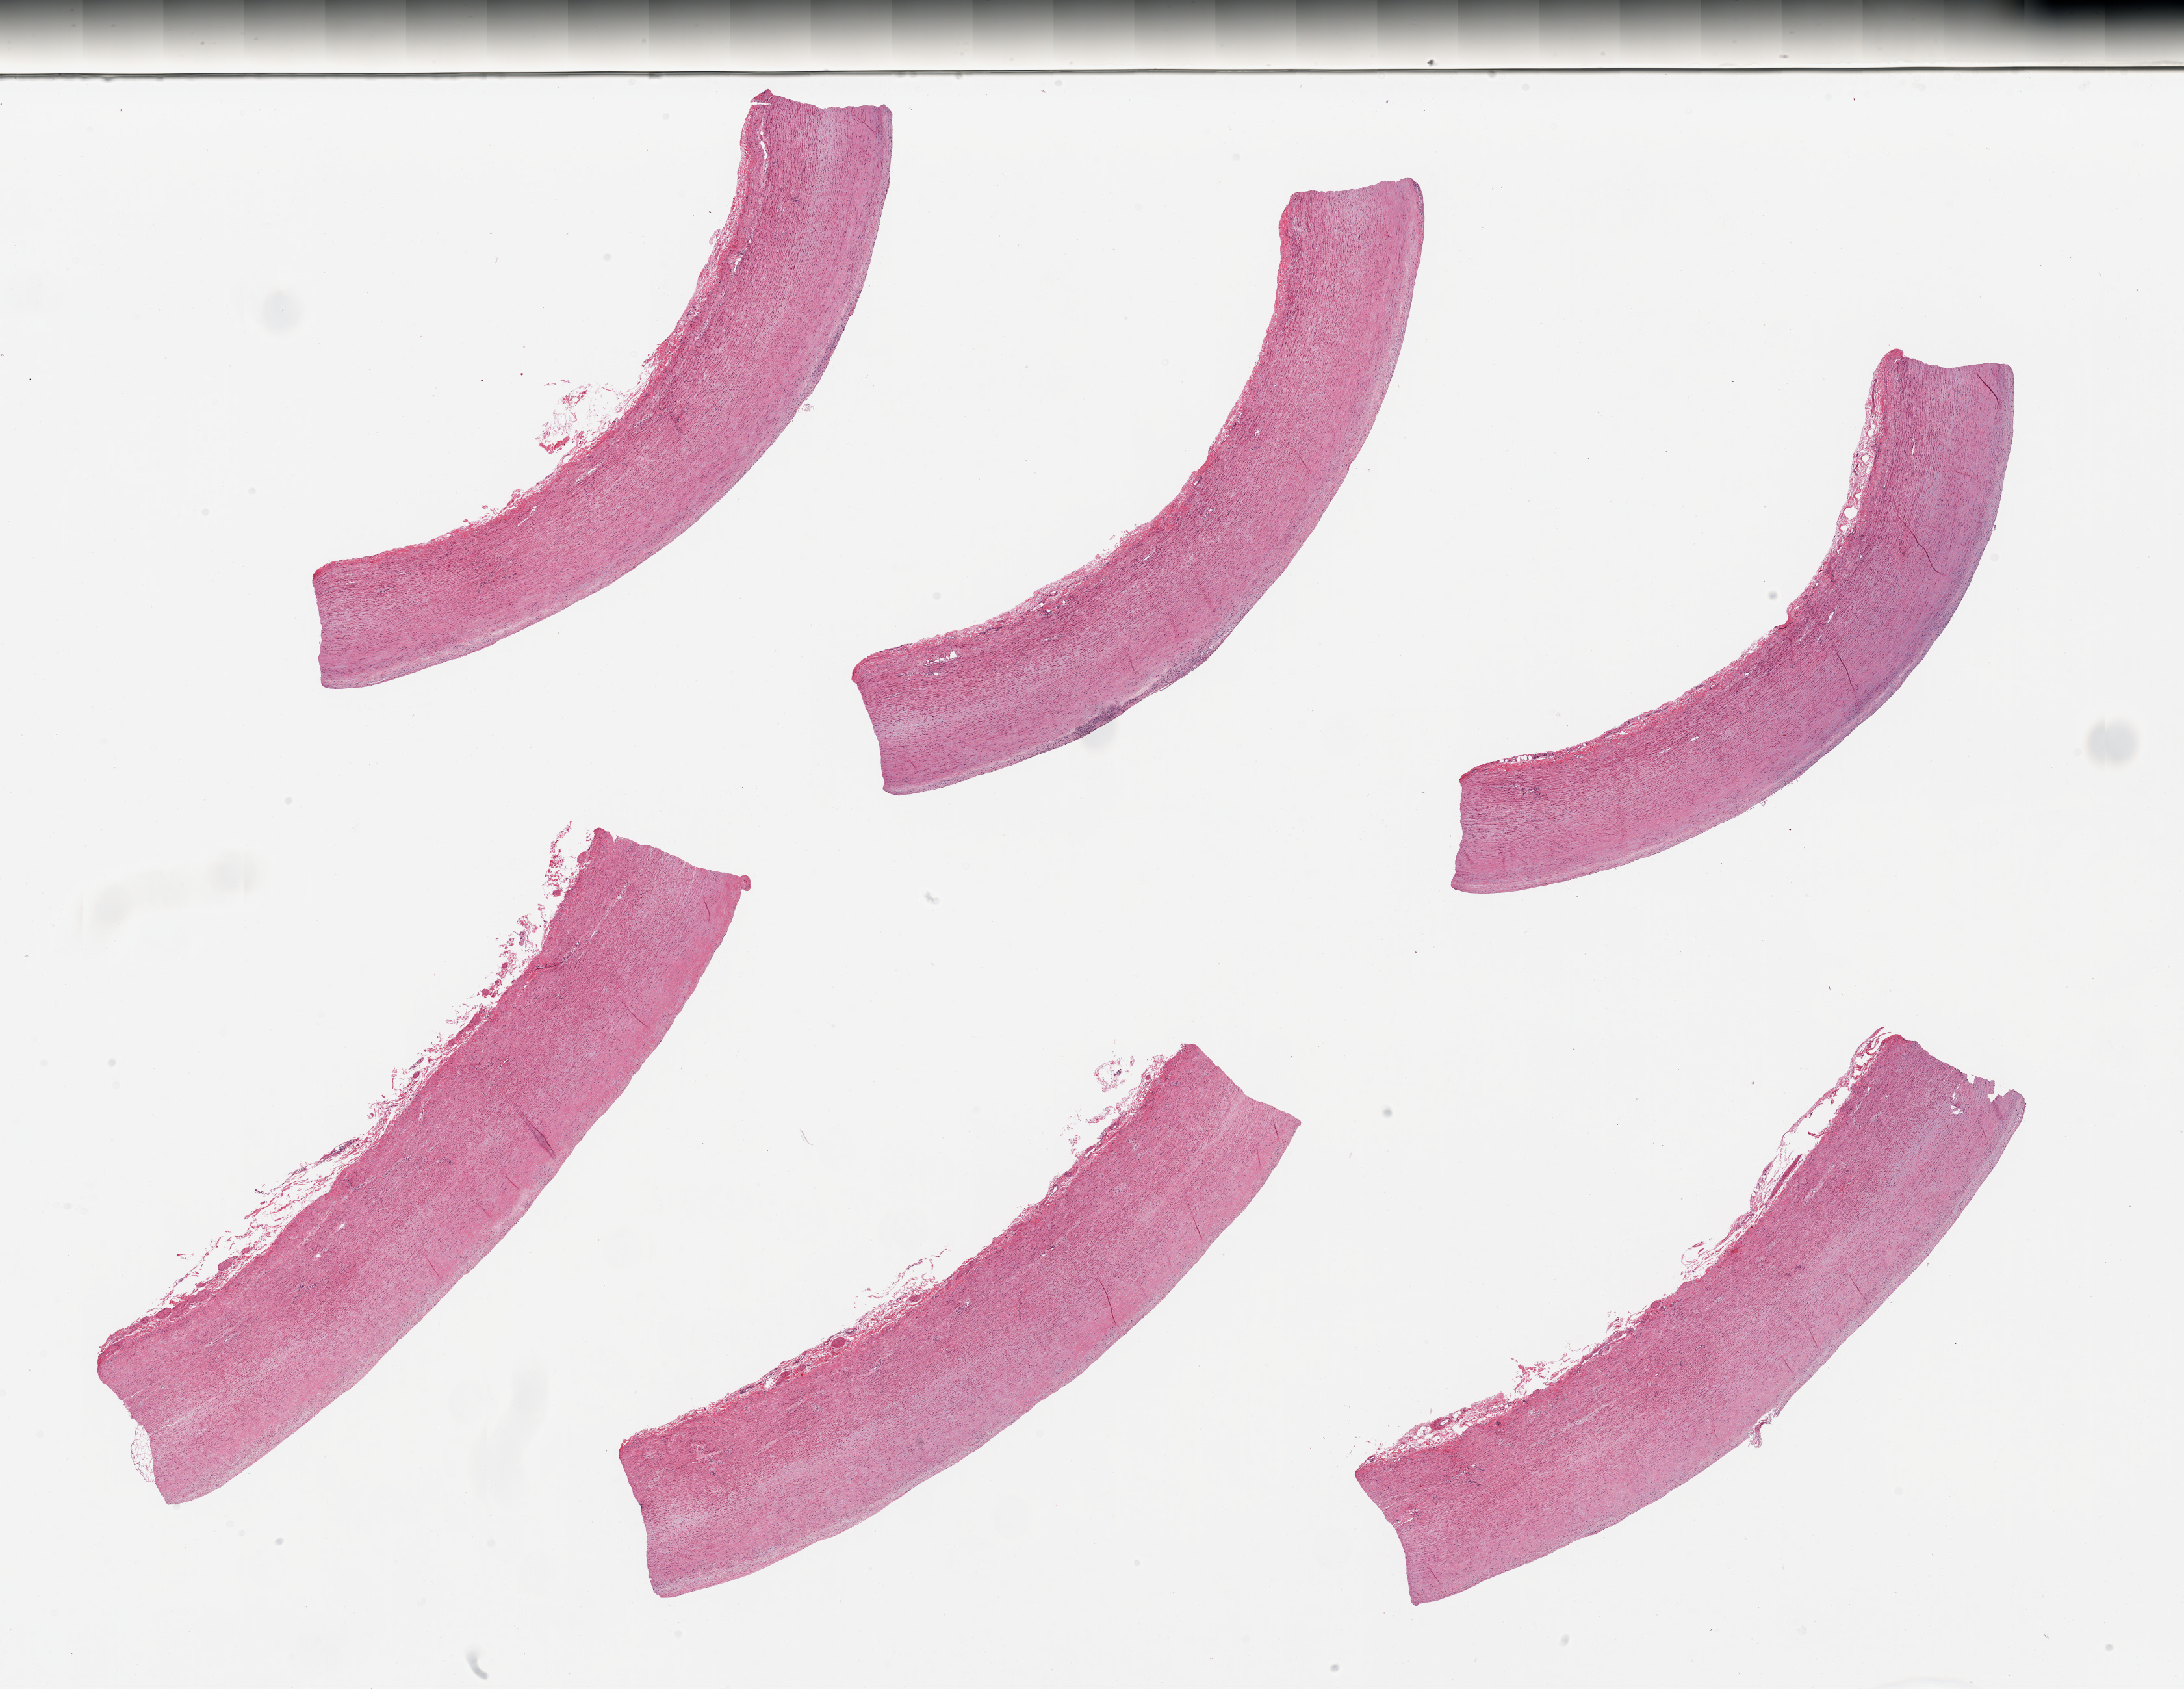
Whole-slide image, hematoxylin and eosin (H&E) stain, whole scanned area (about 26.6 x 20.6 mm, from a 20x scan) shown as a low-resolution overview, PAXgene-fixed paraffin-embedded (PFPE) section, section of aorta (target tissue), donor tissue sample. Female donor.
Reviewer comment on this tissue sample: 6 pieces, minimal atherosis.